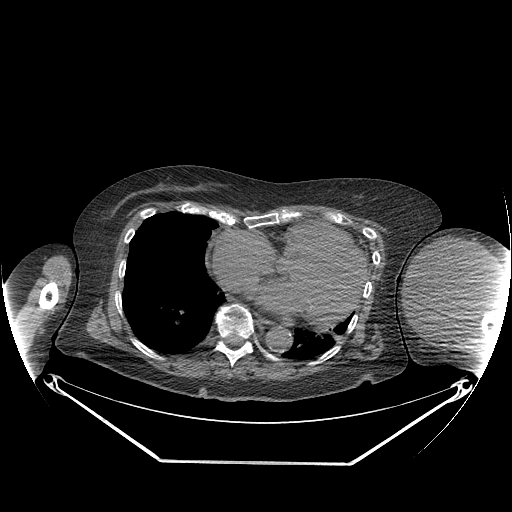
CT of an extremity soft-tissue mass (from a PET/CT study), one axial slice. Position 158 of 267 along the scan axis. Reconstruction kernel STANDARD. 140 kVp. Soft-tissue window (W 400 / L 40 HU). 3.75 mm slice thickness. 512 × 512 image matrix, field of view 500 × 500 mm. Female patient. Case-level facts recorded for this patient, not image findings: histological type: pleiomorphic leiomyosarcoma; grade: high; site of the primary tumour: left biceps.
Annotated regions visible in this slice (expert contour drawn on MRI and transferred to this co-registered scan by the dataset authors):
- gross tumour volume including surrounding oedema: bounding box (x1, y1, x2, y2) in pixels: (404, 237, 496, 330)
- gross tumour volume (mass): (404, 238, 496, 330)